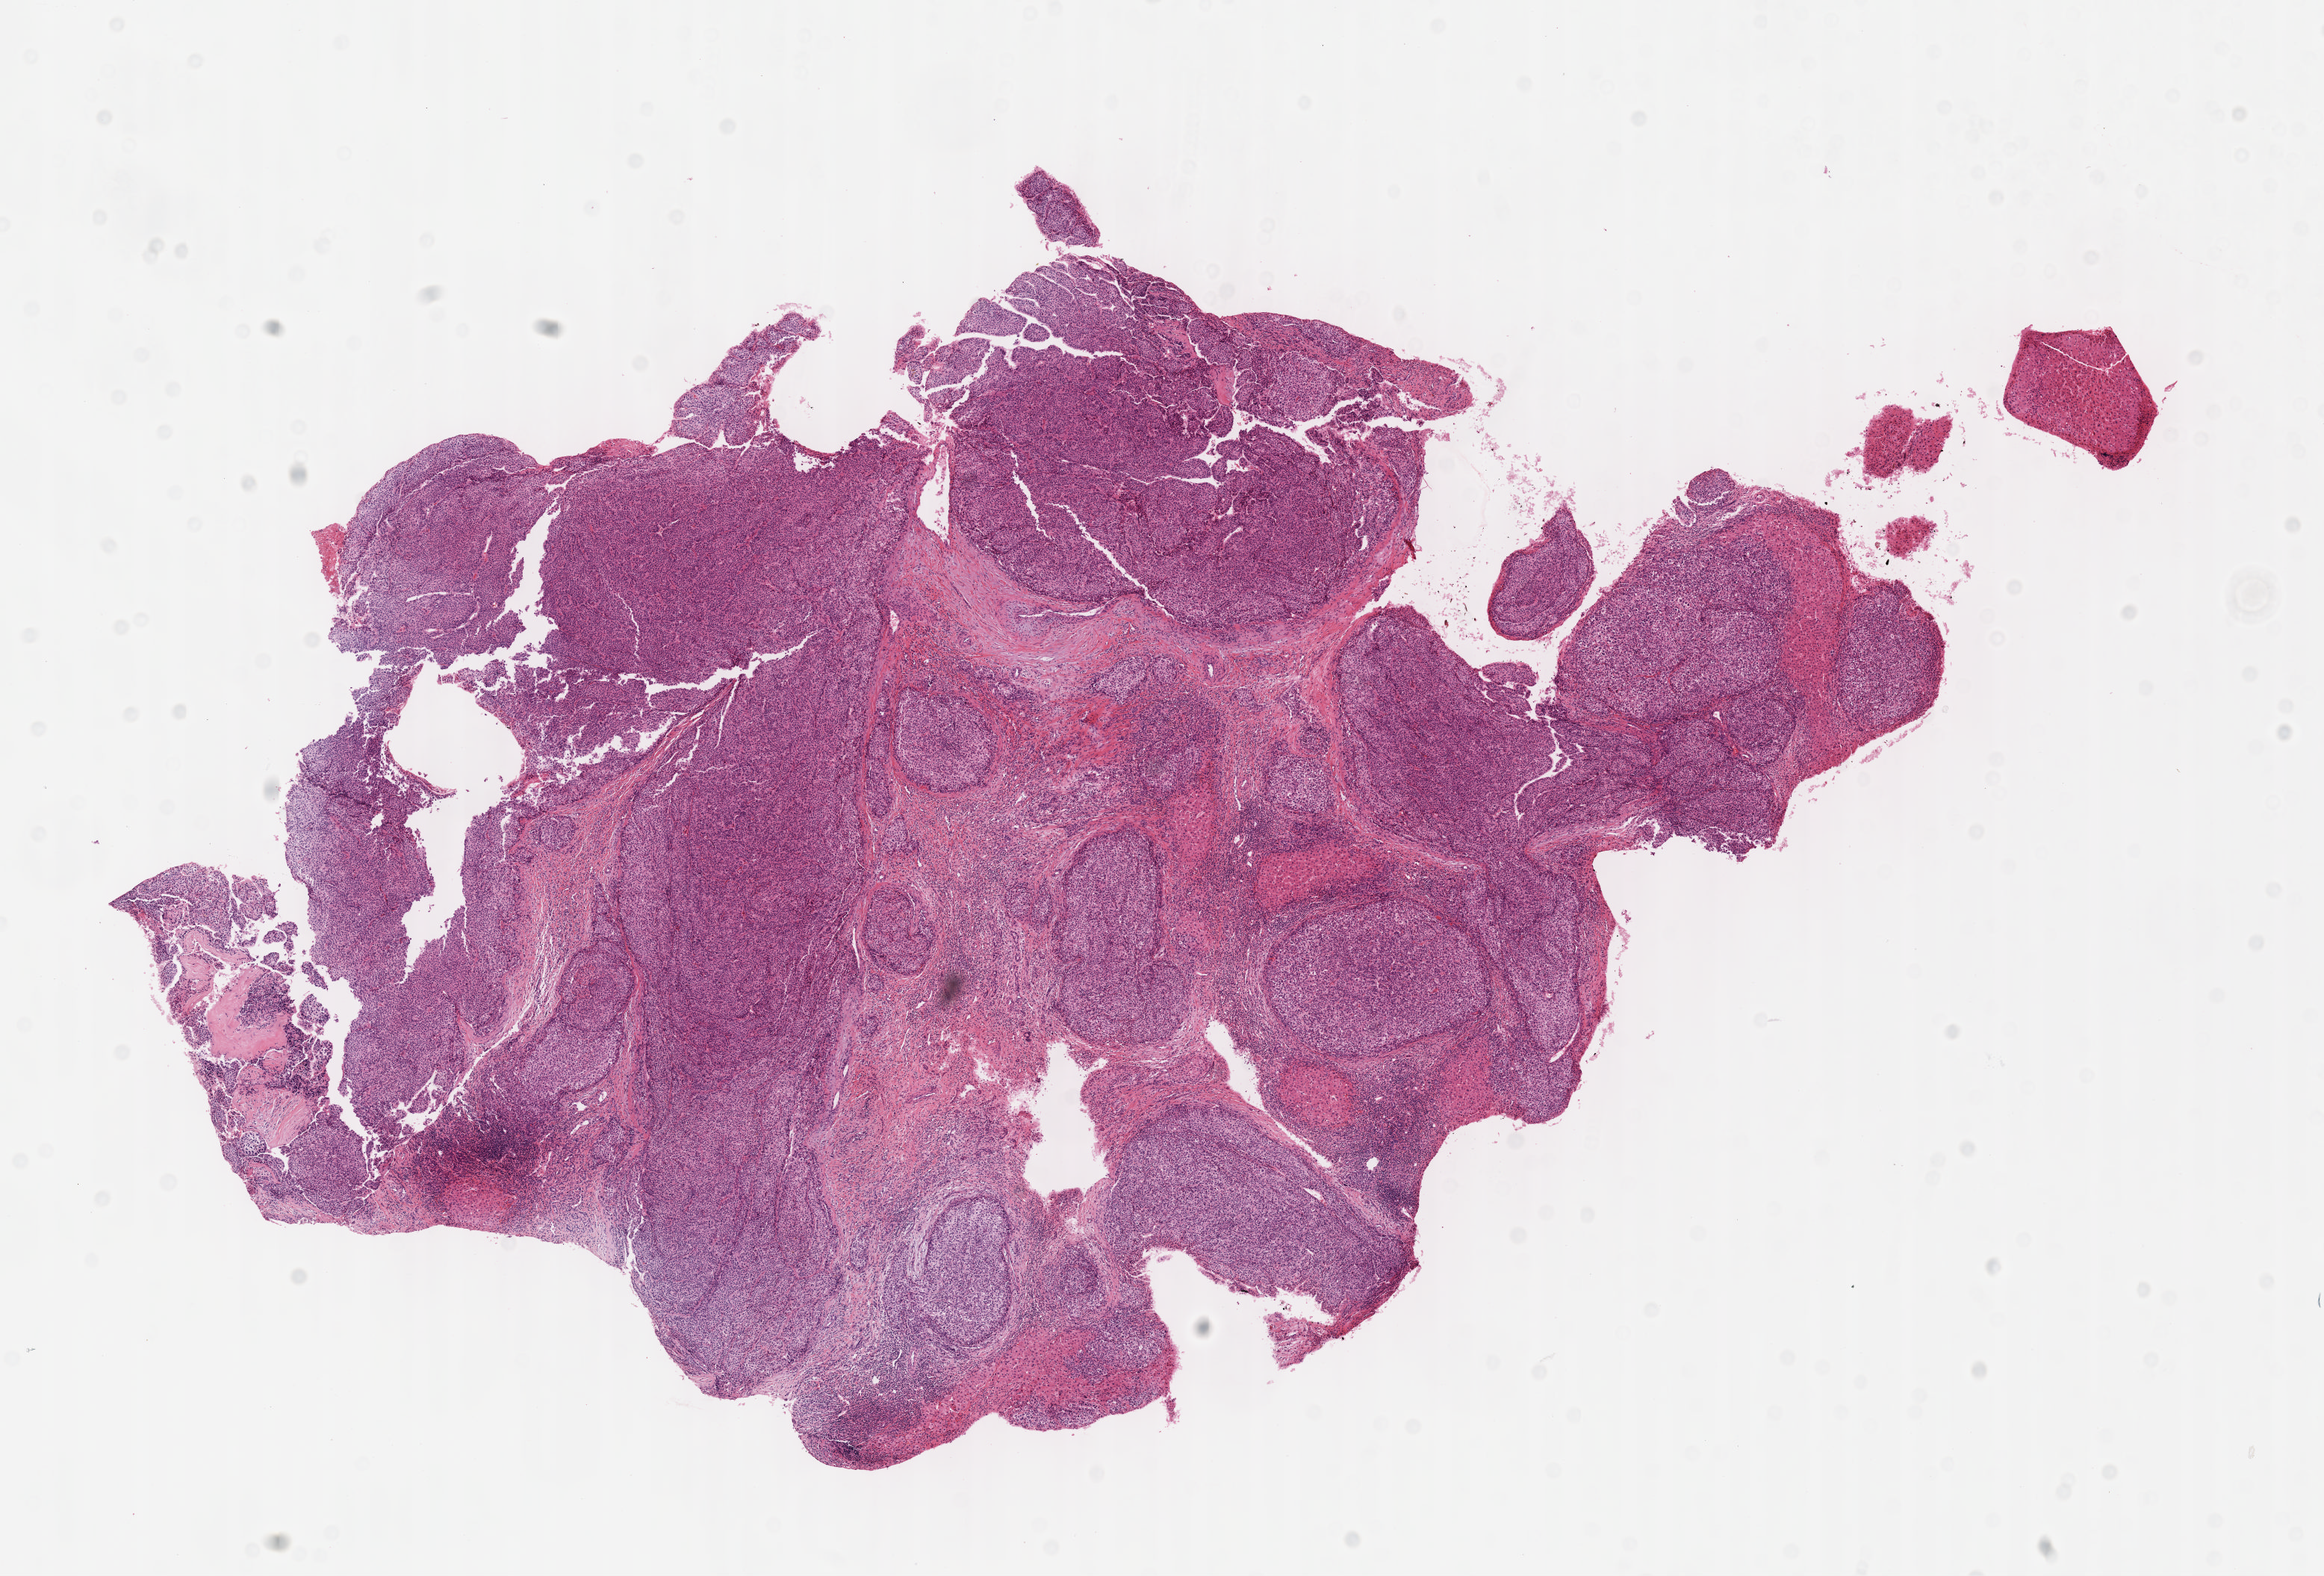
Whole-slide histology image, H&E, whole scanned area (about 12.6 x 8.5 mm) shown as a low-resolution overview, FFPE section, liver, primary tumour sample. Male patient; age at initial diagnosis 45 years. Histologic grade: G3 (poorly differentiated).
Pathologic diagnosis: Hepatocellular carcinoma, NOS. AJCC pathologic stage: I (7th edition).